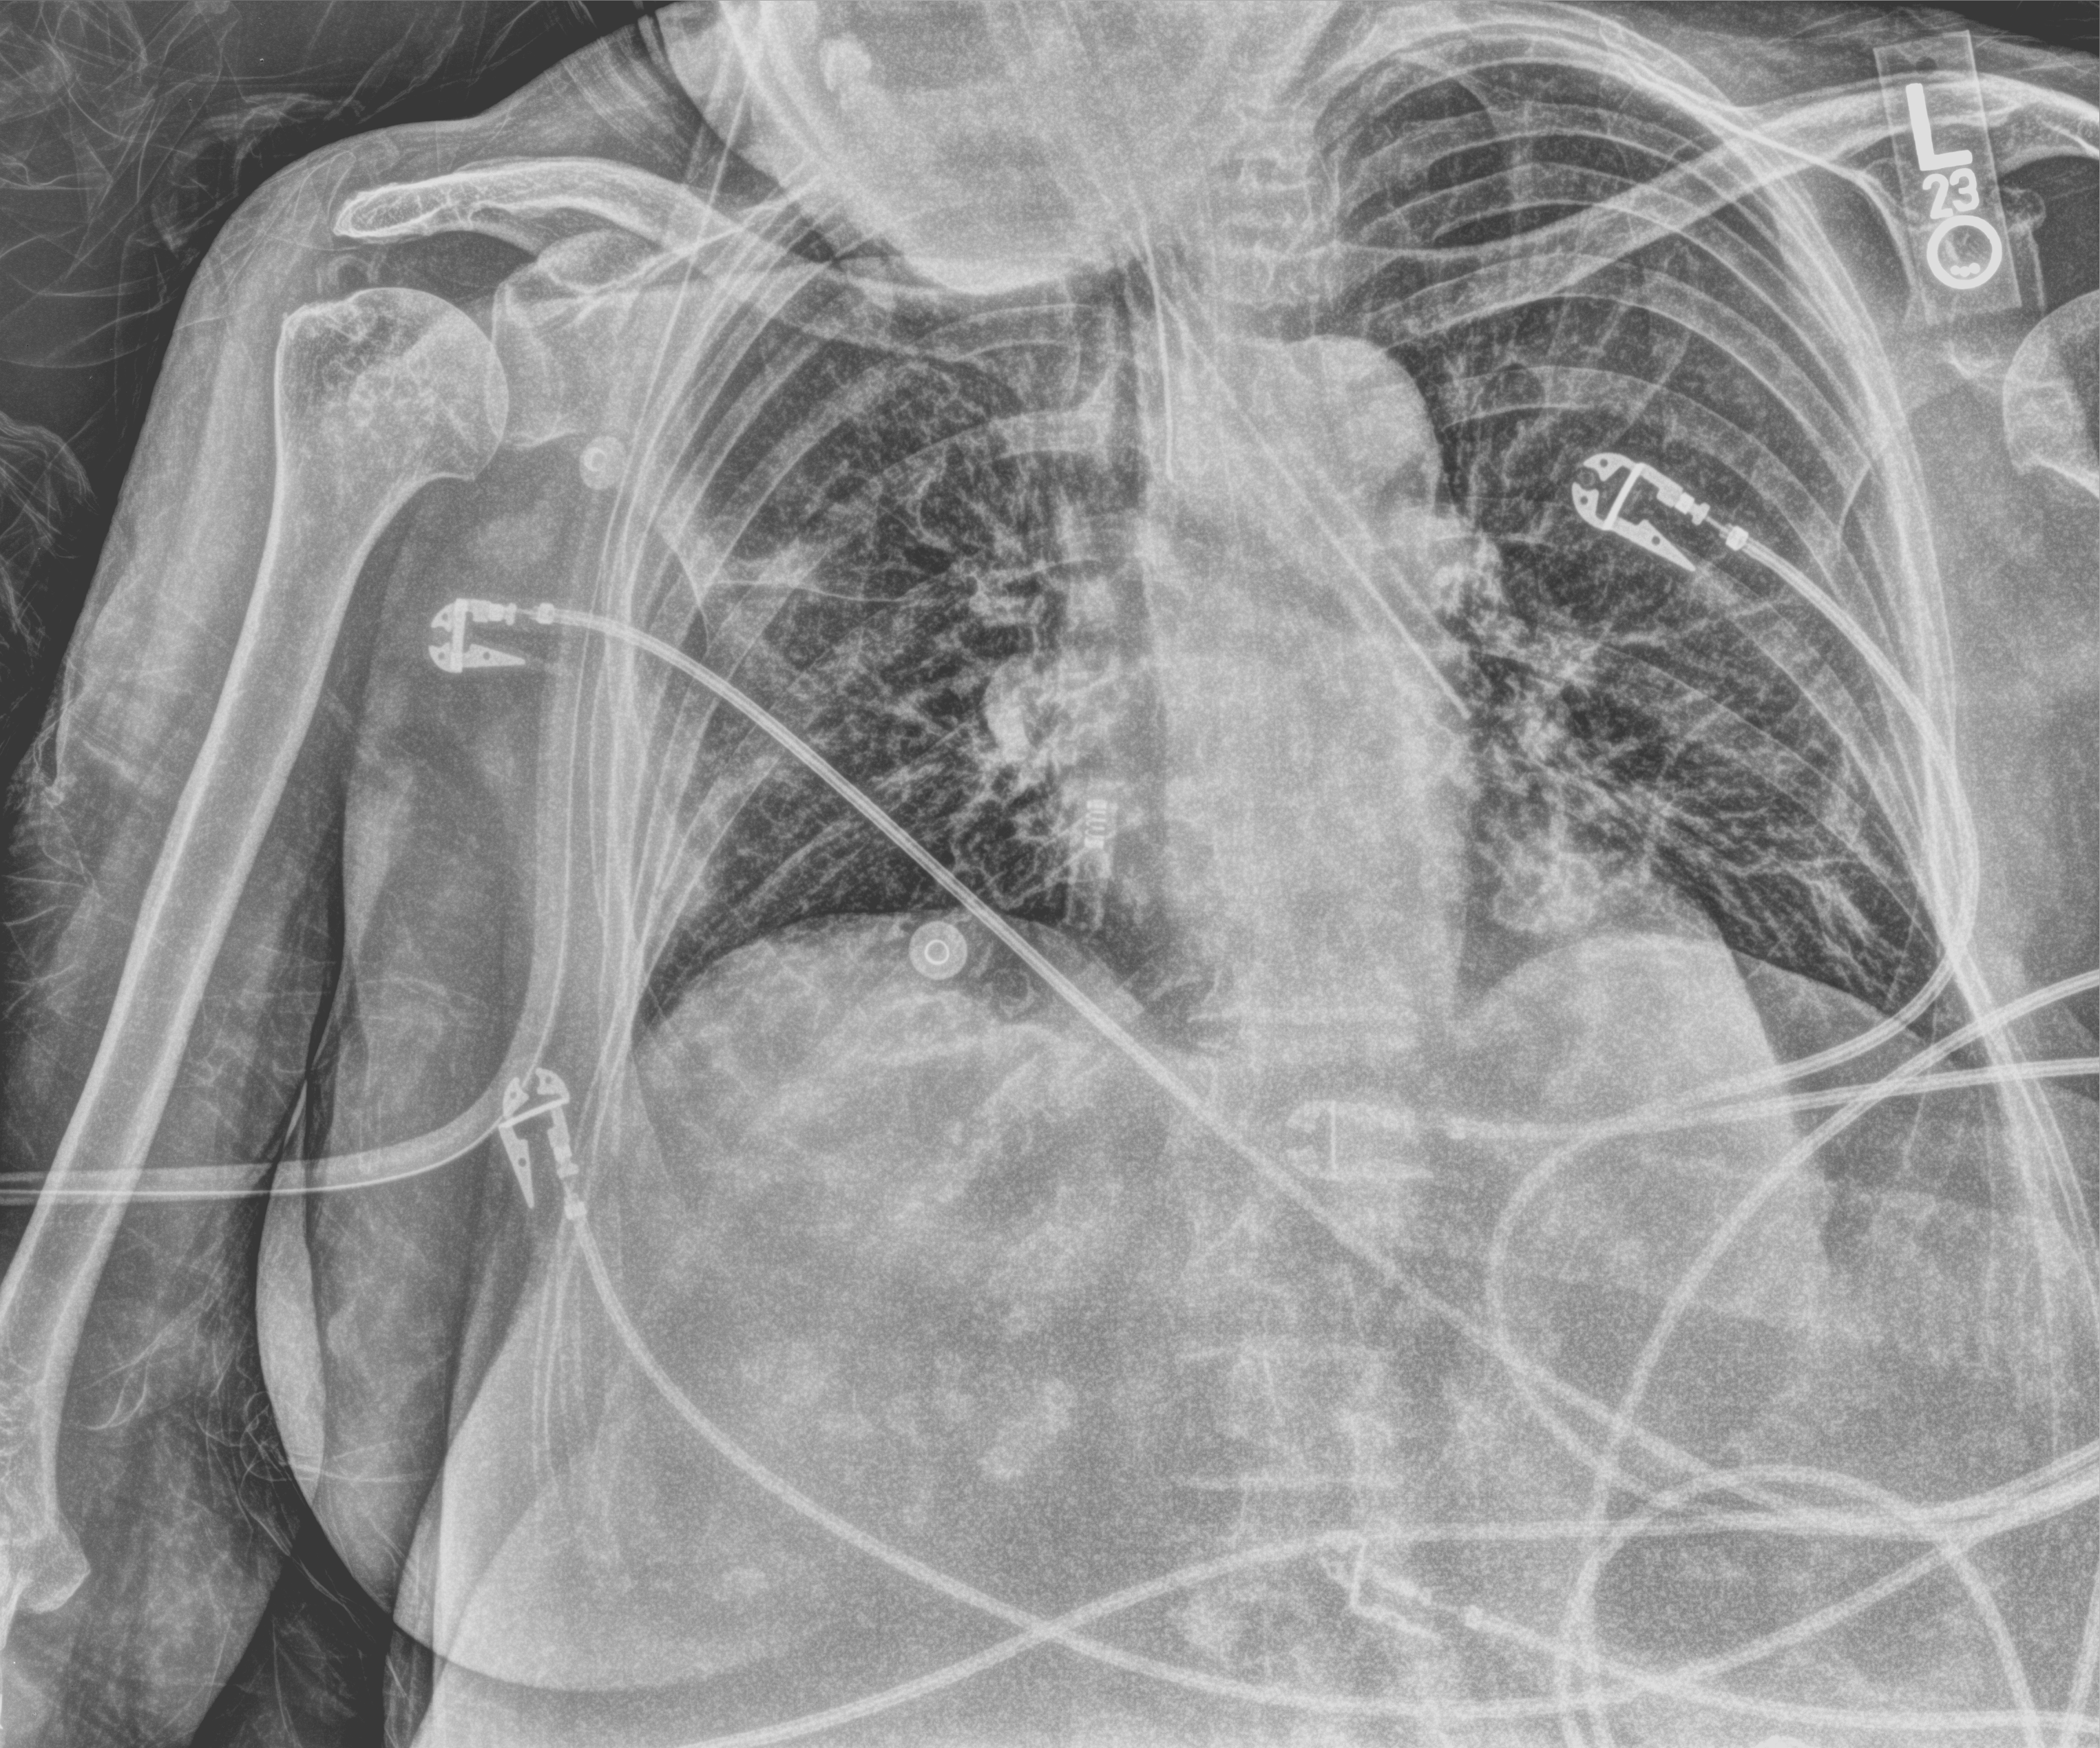
Bedside chest radiograph (computed radiography); anteroposterior (AP) projection. Female patient hospitalised with COVID-19, age 75–90 years.
Hospital-stay facts (about this admission, not read from this image; timing relative to this image not recorded): mechanically ventilated during this hospital stay: yes; chronic kidney disease (admission record): yes.